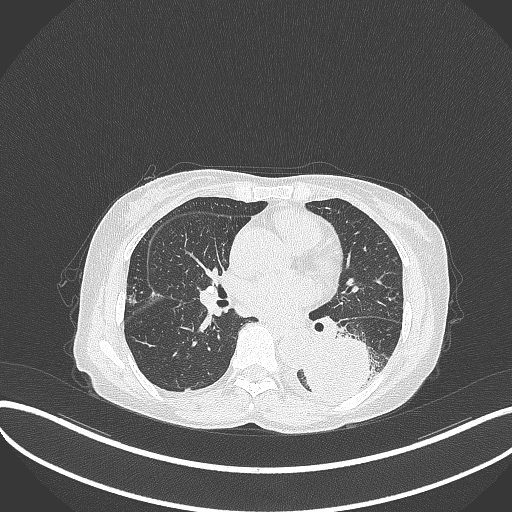
Chest CT, one axial slice; slice 153 of 370 in the series (ordered by position); 120 kVp; lung window (W 1500 / L -600 HU); 1 mm slice thickness; 512 × 512 image matrix, field of view 400 × 400 mm. Female patient, age 78 years. Case-level facts recorded for this patient, not image findings: clinical TNM (as recorded): T3 N0 M1.
Outlined on this slice (rectangle marked by the reading radiologist):
- lung tumour (recorded histology: squamous cell carcinoma): bounding box [x1, y1, x2, y2] px = [301, 324, 384, 400]